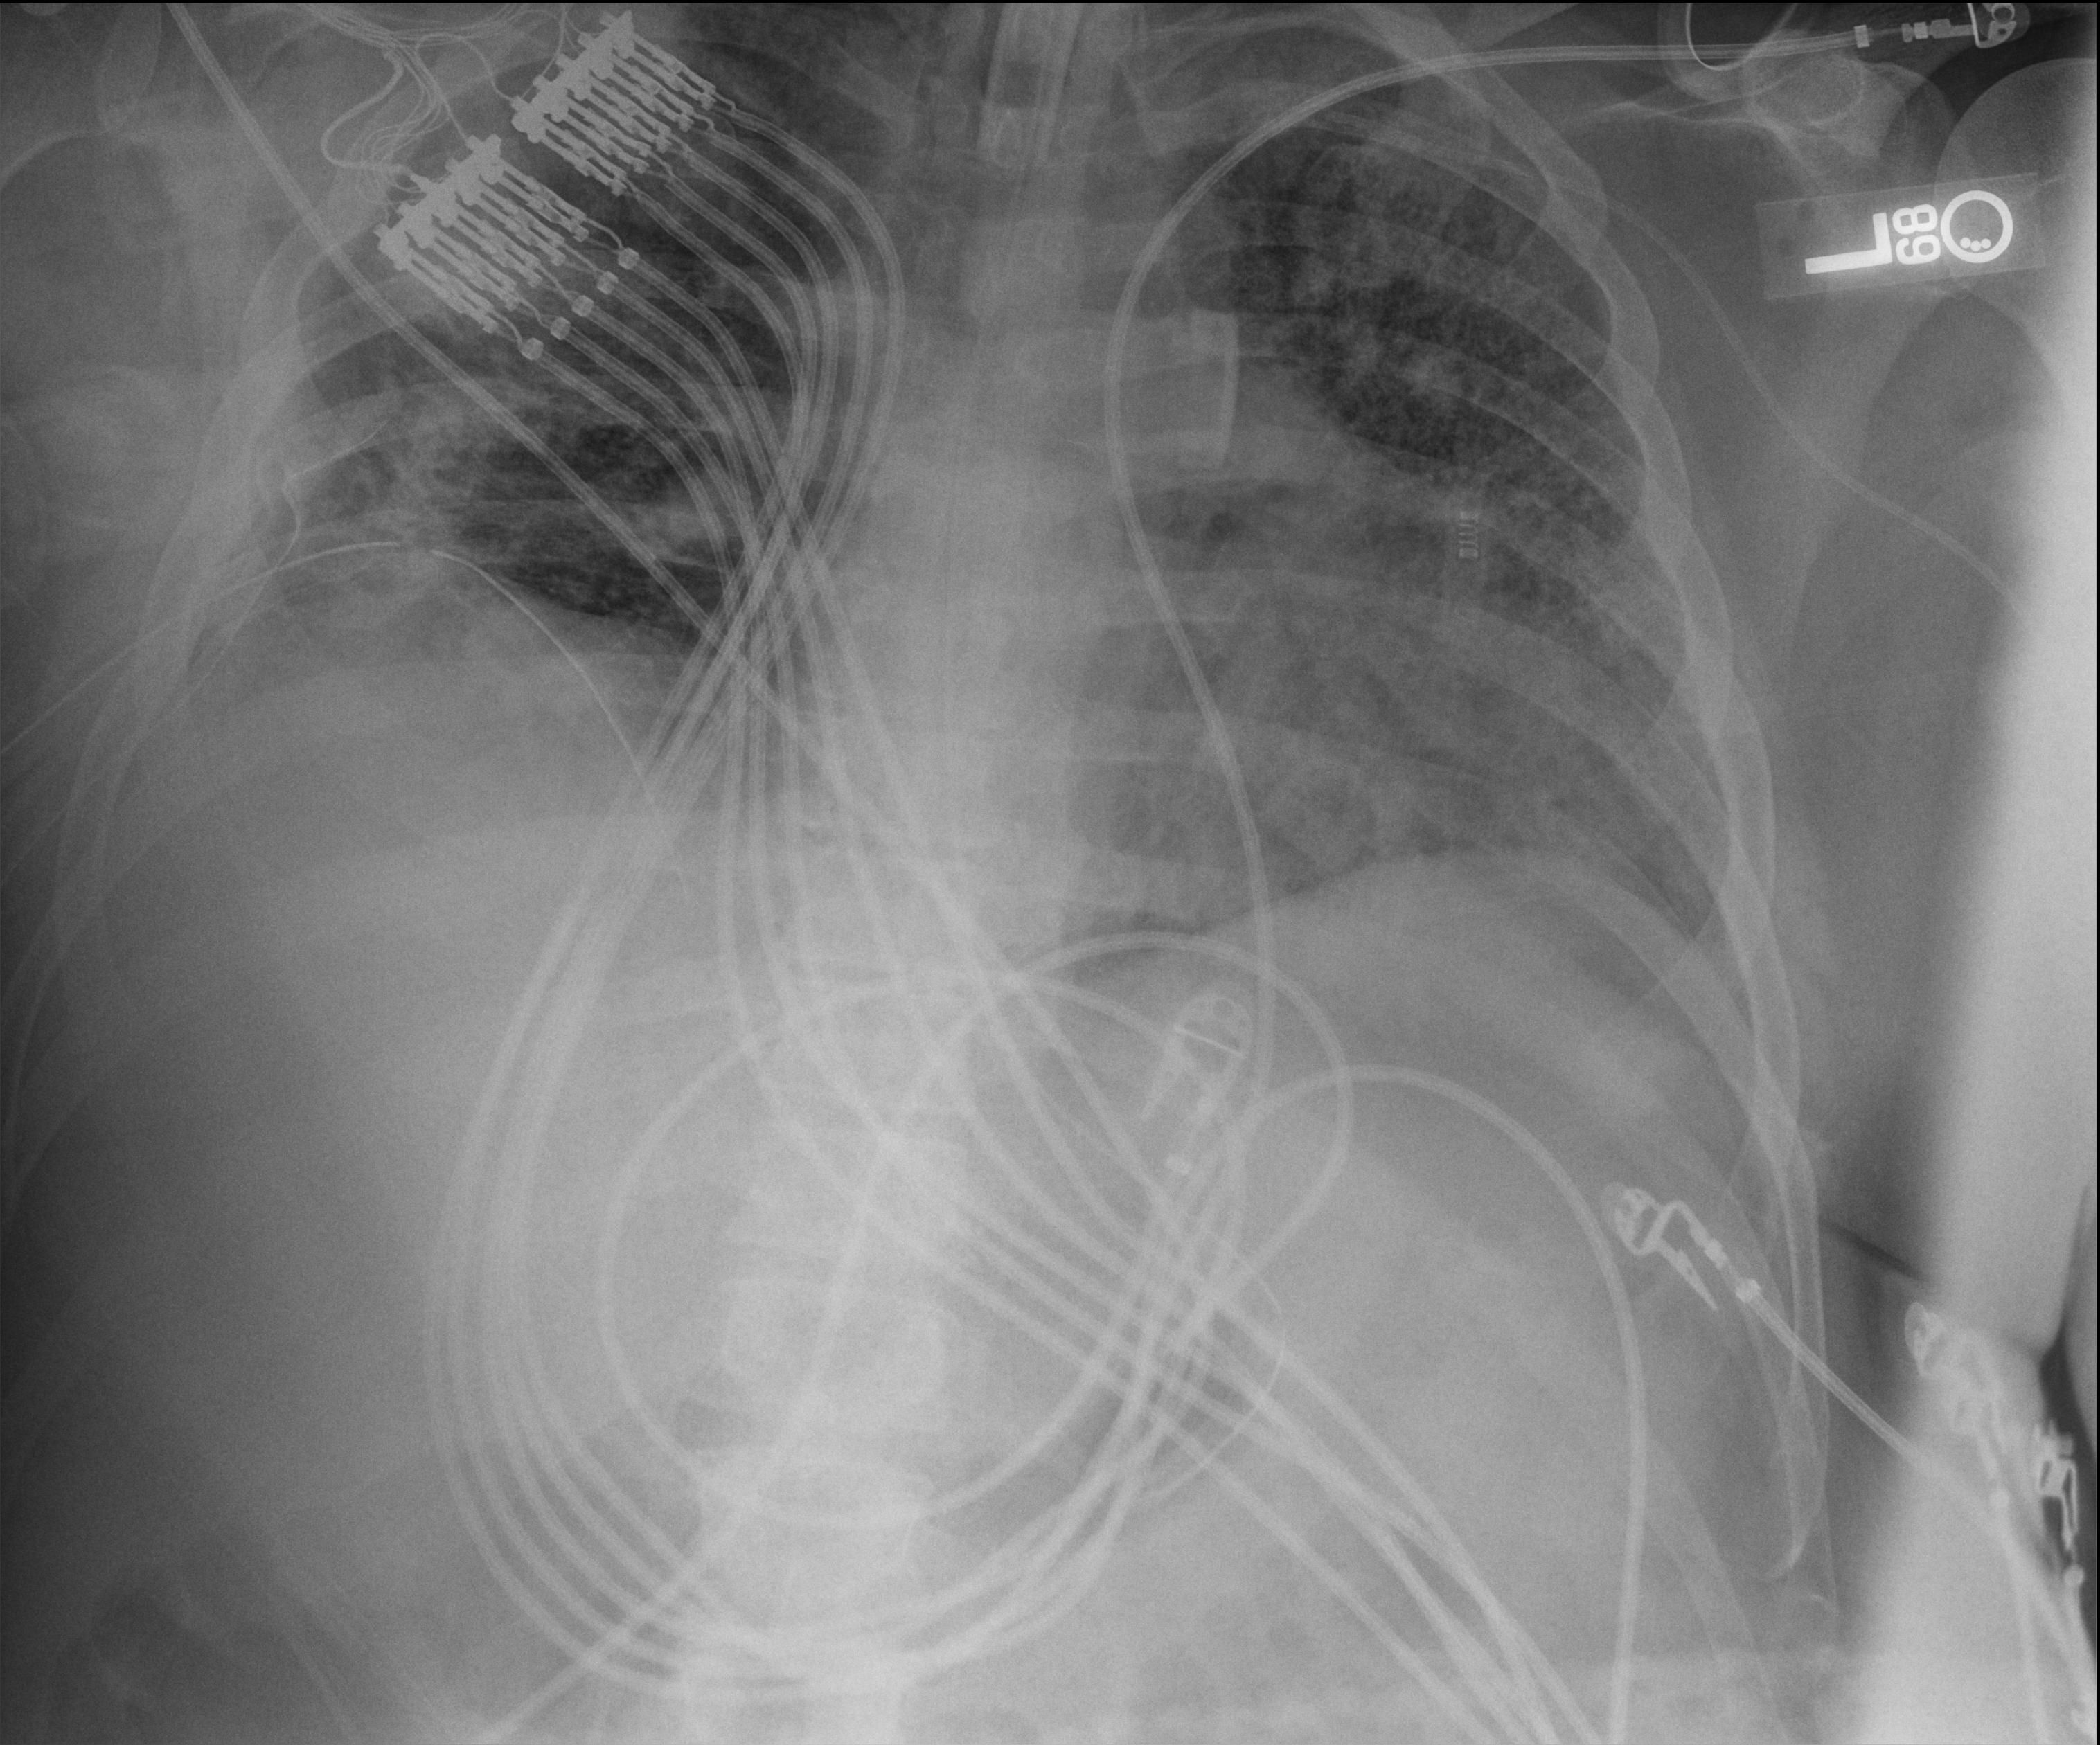
Chest X-ray. Male patient hospitalised with COVID-19, age 18–59 years.
Admission-level facts for this patient (not findings on this image; timing relative to this image not recorded): other chronic lung disease (admission record): no.